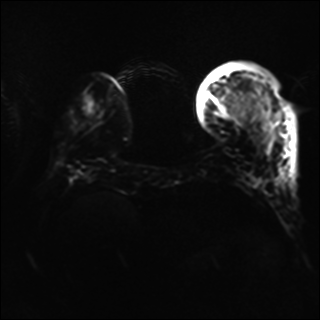
Breast MRI, one axial slice; position 11 of 40 along the scan axis; diffusion-weighted series; image 2 of 4 stored at this slice position (different b-values; order by instance number); 1.5 T; 4 mm slice thickness; 320 × 320 image matrix, field of view 320 × 320 mm. Female patient.
Outlined on this slice (expert manual segmentation):
- tumour on diffusion-weighted imaging: bounding box <244,107,254,115> (left, top, right, bottom; pixels)